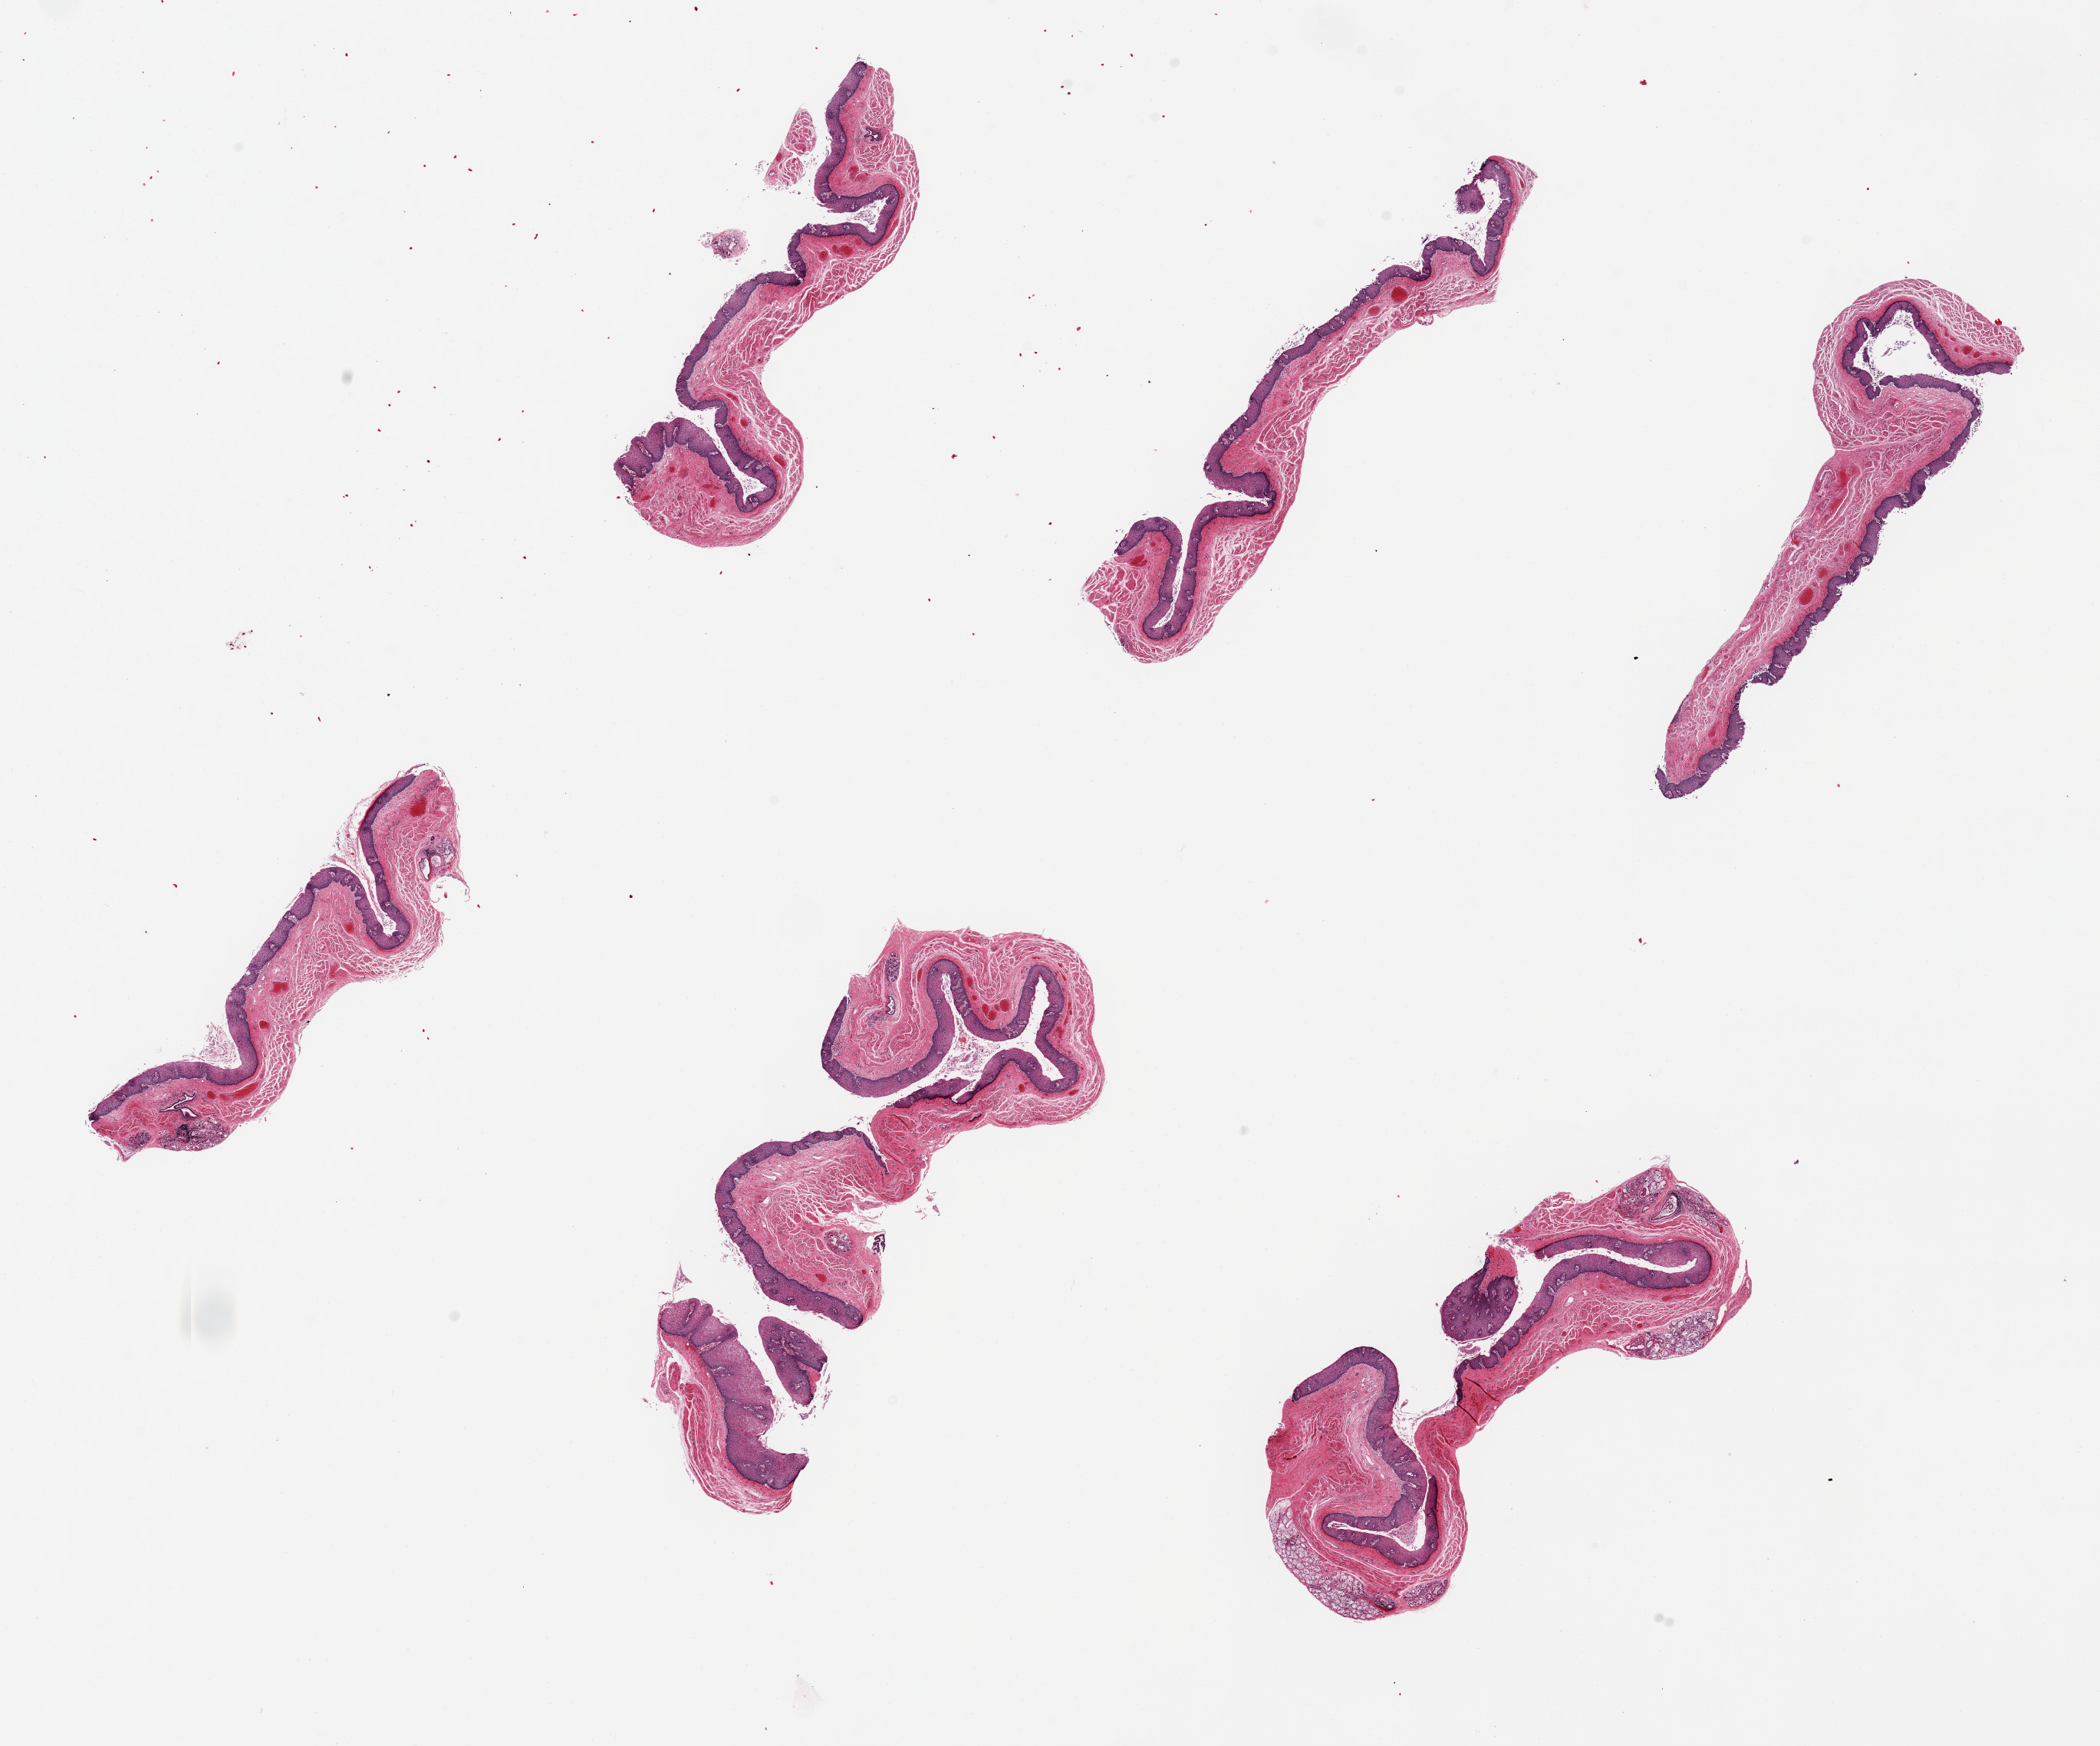
Haematoxylin and eosin whole-slide image — shown as a low-resolution overview of the whole scanned area (about 21.7 x 18.0 mm, slide scanned at 20x). PAXgene-fixed paraffin-embedded (PFPE) section. Section of esophageal mucous membrane (target tissue). Donor tissue sample.
Pathologist's review note for this sample: 6 pieces up to 7x3mm; squamous mucosa ~15% thickness.